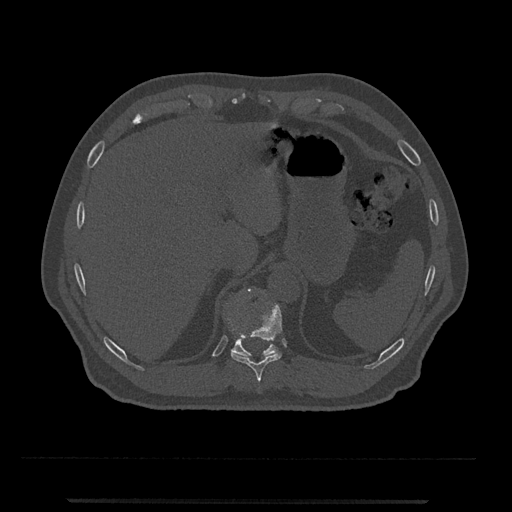
CT including the spine, one axial slice. Slice 497 of 797 in the series (ordered by position). 120 kVp. Bone window (W 1800 / L 400 HU). 0.5 mm slice thickness. 512 × 512 image matrix, field of view 419 × 419 mm. Male patient, age 63 years. Case-level facts recorded for this patient, not image findings: primary cancer: prostate.
Structures marked on this image (semi-automatic segmentation, software-assisted and operator-edited):
- T10 vertebra: bounding box <231,291,283,382> (left, top, right, bottom; pixels)
- T11 vertebra: <228,288,278,356>